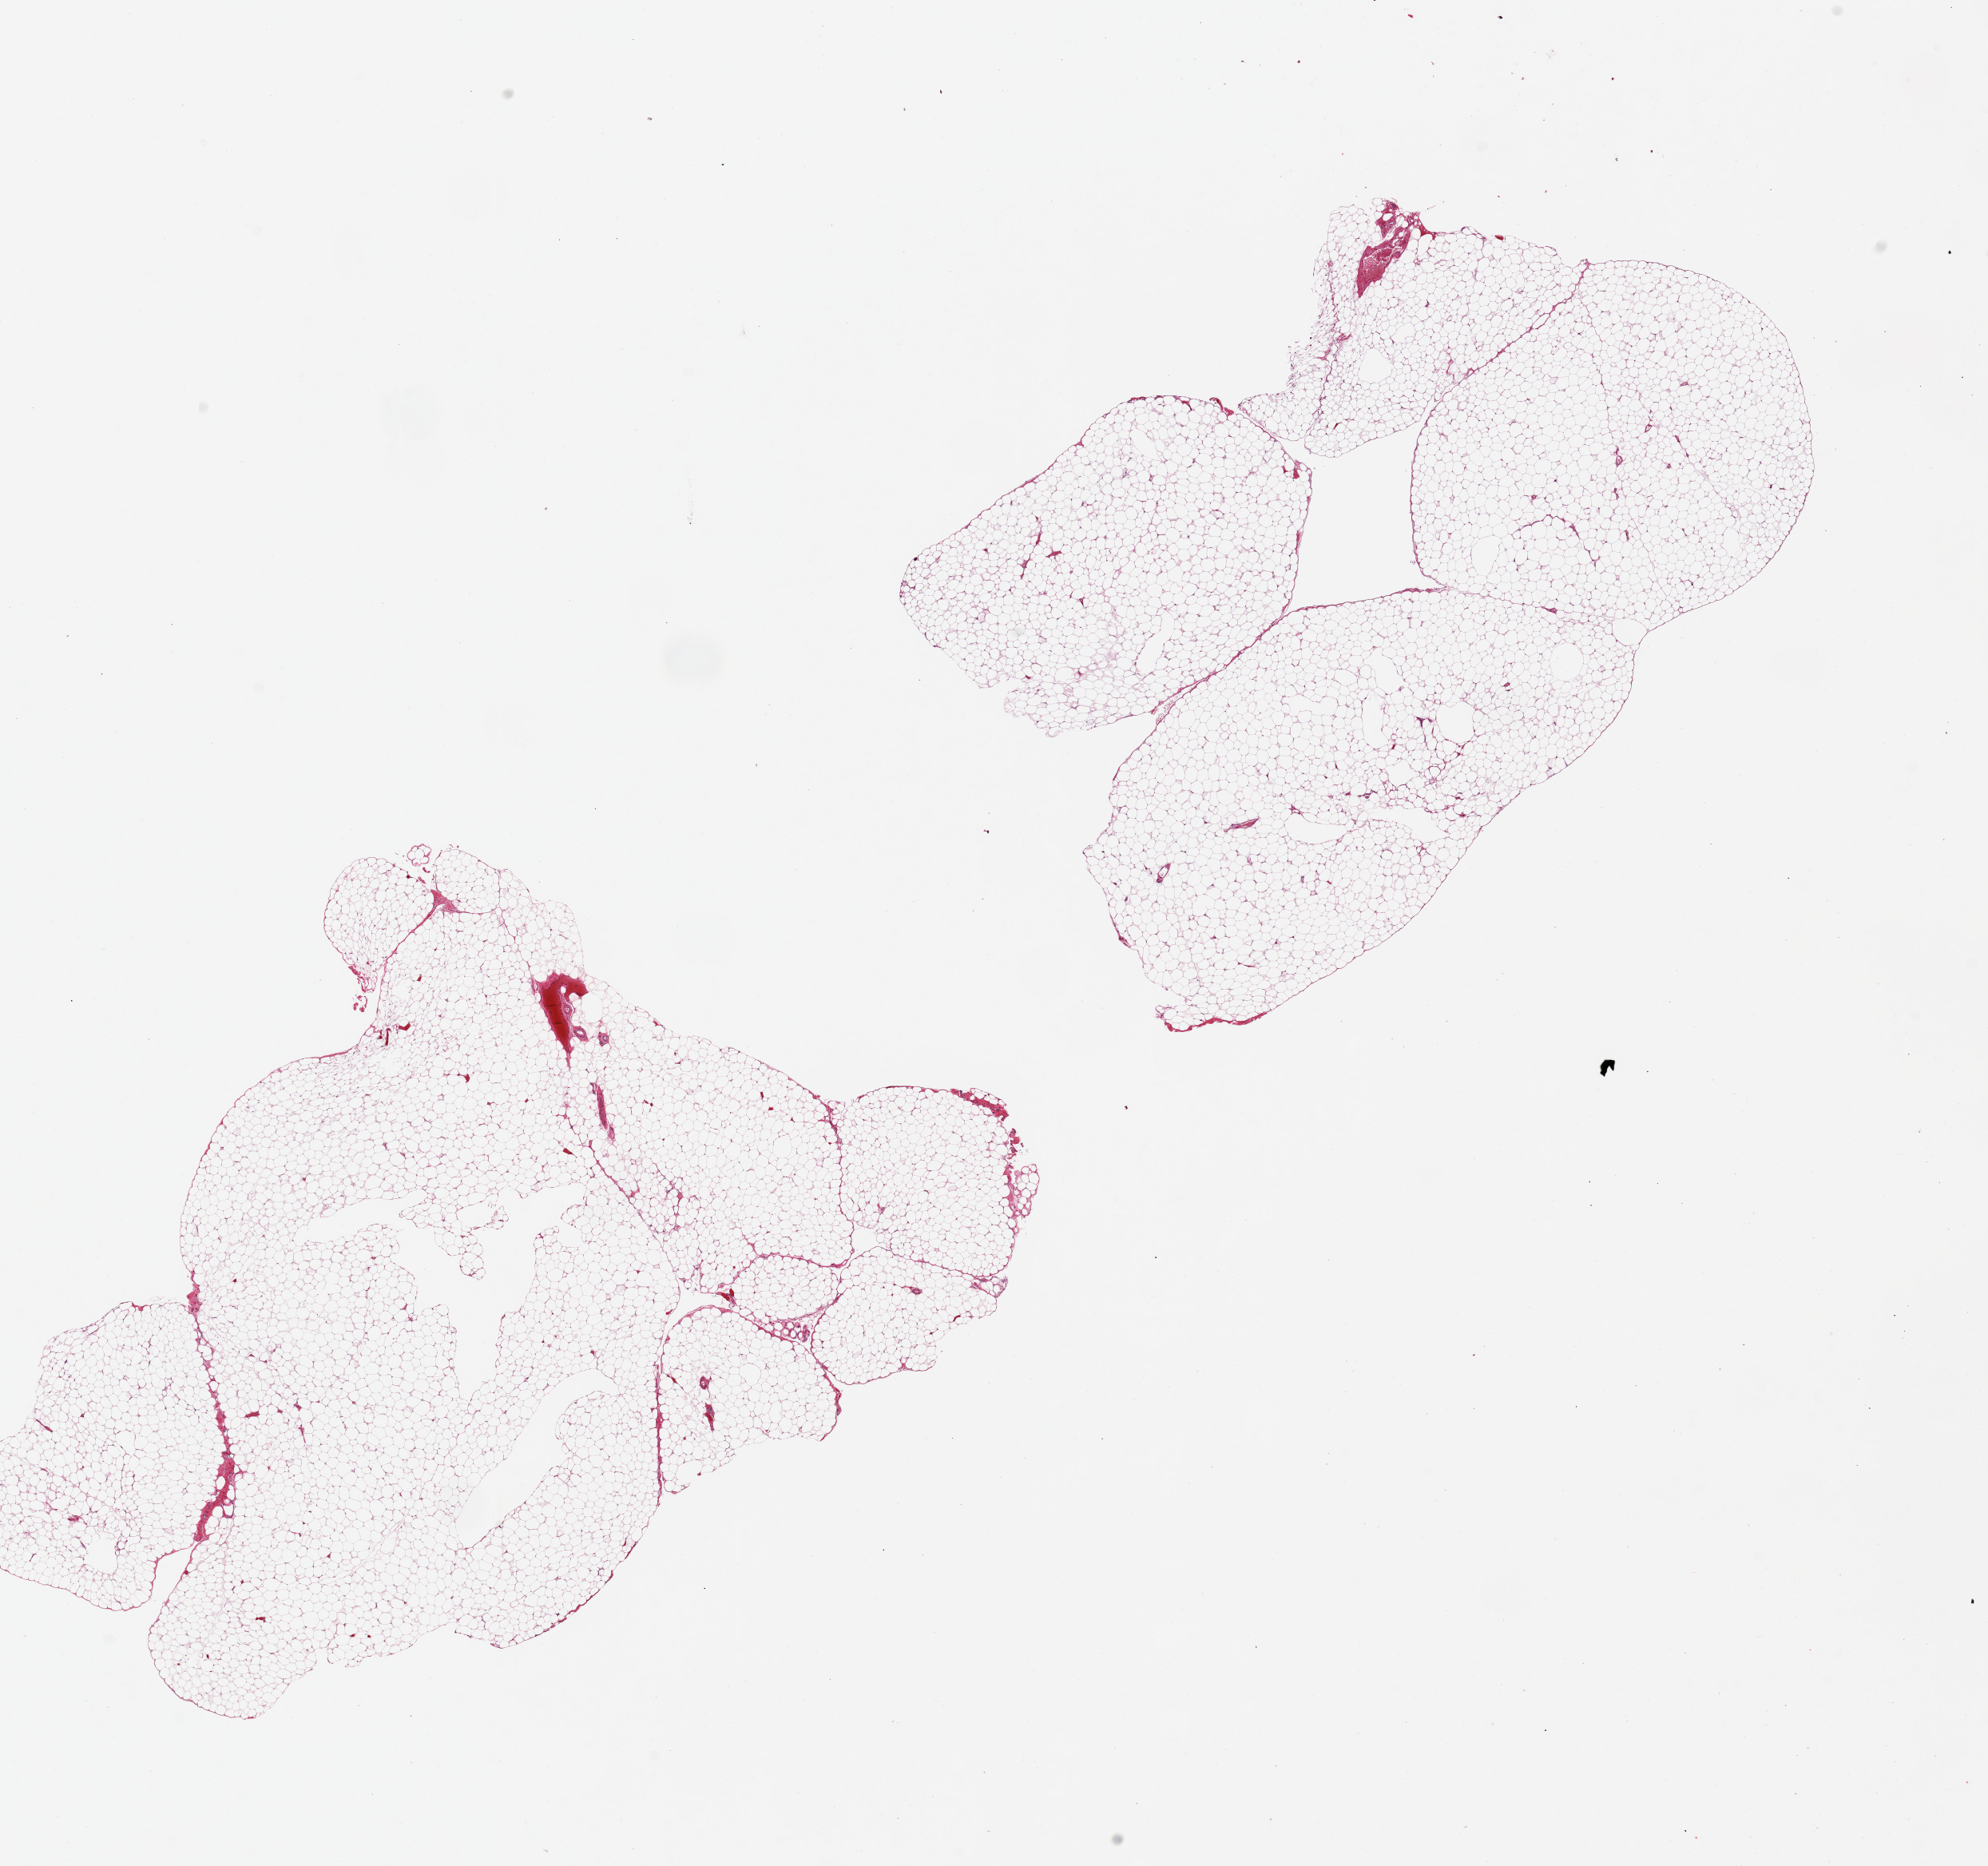
Haematoxylin and eosin whole-slide image, shown as a low-resolution overview of the whole scanned area (about 19.7 x 18.5 mm), PAXgene-fixed paraffin-embedded (PFPE) section, section of omentum (target tissue), donor tissue sample. Male donor.
Pathologist's review note for this sample: 2 pieces ~9x6mm.